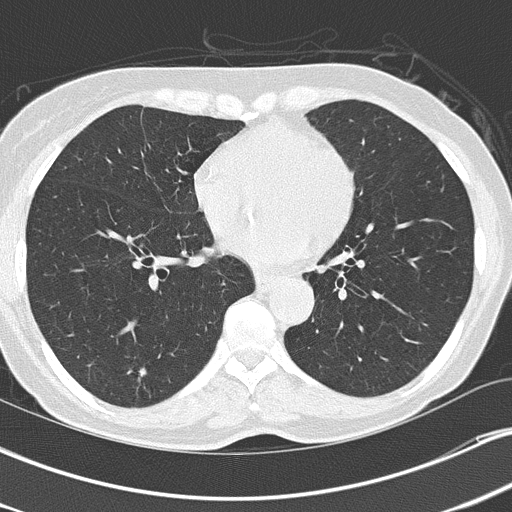
Axial slice from a low-dose chest CT screening exam. Second annual screen. Lung window (W 1500 / L -600 HU). 2 mm slice thickness. Lung (sharp) reconstruction kernel (B50f). Female participant, aged 67 years at enrolment. Current smoker at enrolment.
- Lesion marked by an expert reader, box from (x=128, y=363) to (x=160, y=389) px.
- The screening reader recorded 2 non-calcified nodules or masses ≥4 mm on this exam (right lower lobe, left lower lobe); which of them this box marks is not recorded.
- Lung cancer was diagnosed 507 days after this screen (after the third annual screen): adenocarcinoma, NOS, left lower lobe, poorly differentiated (G3), stage IA (AJCC 6th edition), 25 mm at pathology.